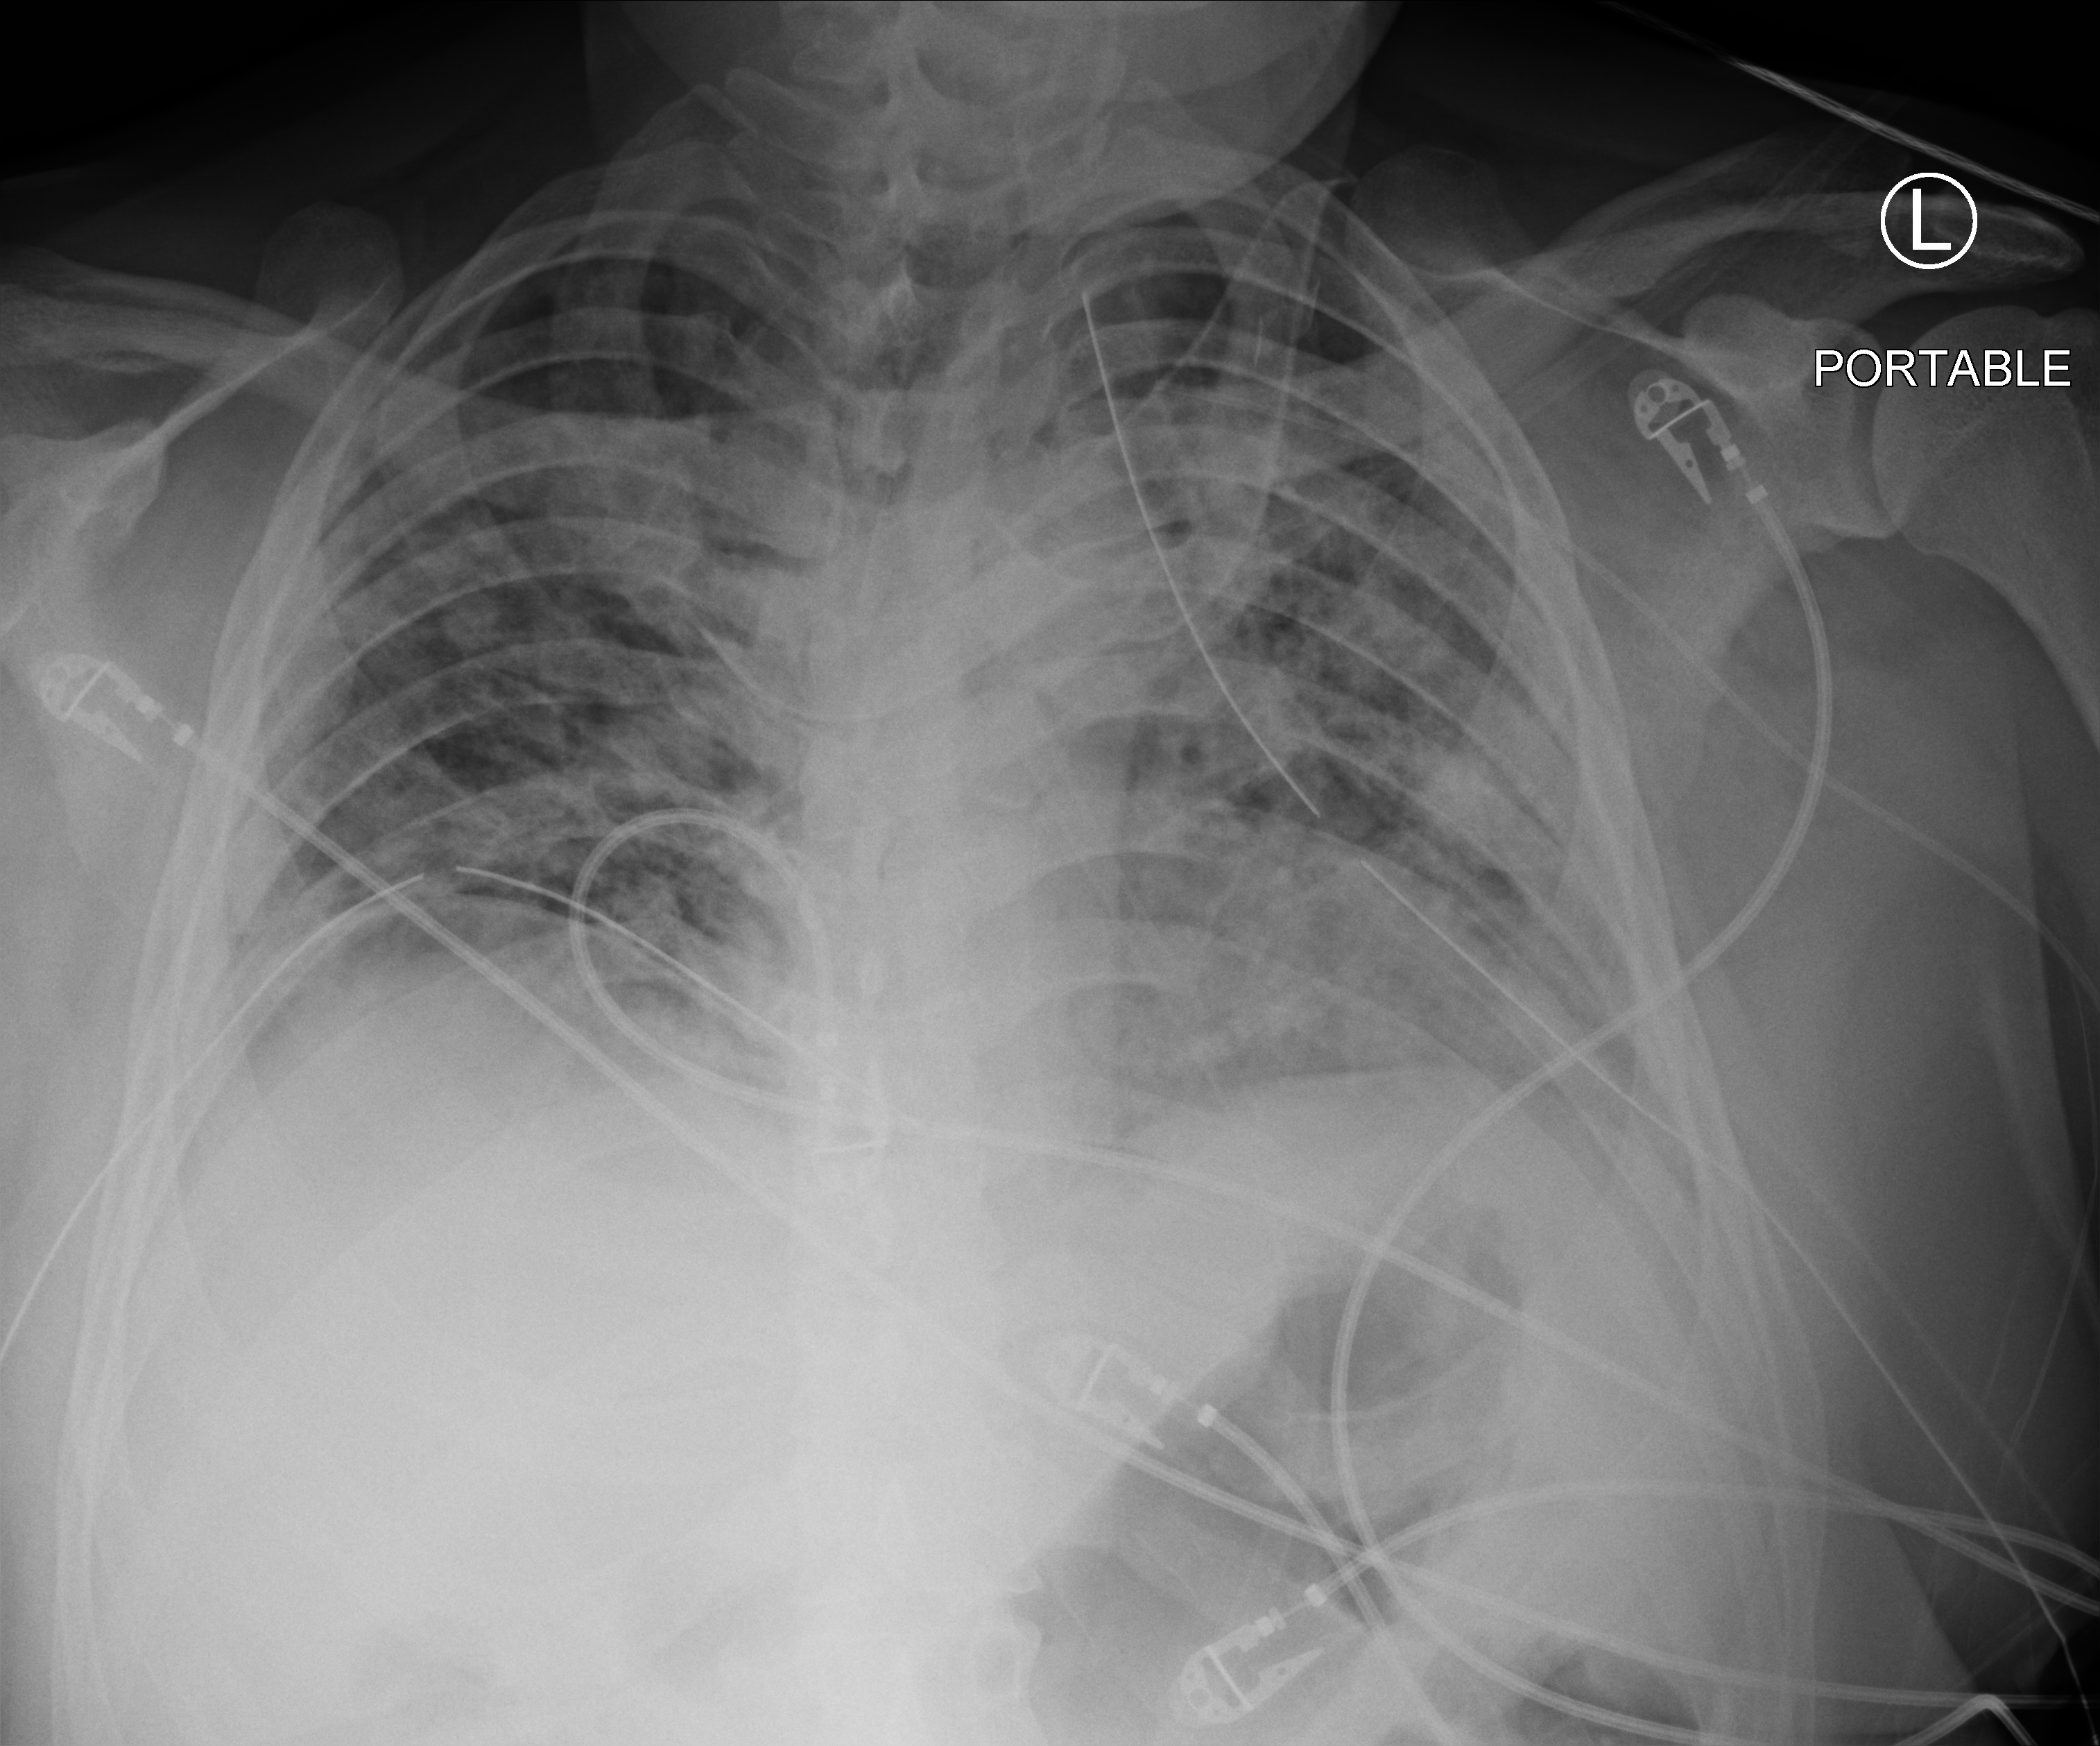
Chest X-ray (portable); anteroposterior (AP) projection. Patient hospitalised with COVID-19; male, aged 18–59 years.
Hospital-stay facts (about this admission, not read from this image; timing relative to this image not recorded): admitted to intensive care during this hospital stay: yes.